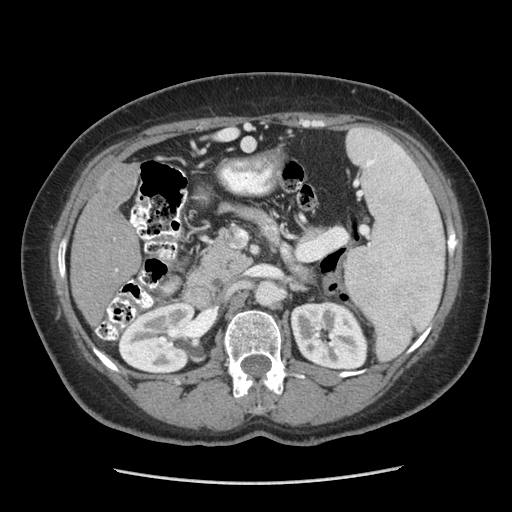
Contrast-enhanced abdominal CT (liver protocol), one axial slice. Slice 135 of 185 in the series (ordered by position). Soft-tissue window (W 400 / L 40 HU). 2.5 mm slice thickness. 512 × 512 image matrix, field of view 360 × 360 mm. Case-level facts recorded for this patient, not image findings: diagnosis: hepatocellular carcinoma (patient treated with transarterial chemoembolisation; whether this scan precedes or follows treatment is not stated here); TNM stage (as recorded): Stage-I; Child-Pugh class: A; tumour nodularity: uninodular.
Outlined on this slice (semi-automatic segmentation, software-assisted and operator-edited):
- liver parenchyma outside the tumour (the mass and vessels are separate outlines, so this box may not span the whole liver): bounding box (x1, y1, x2, y2) in pixels: (70, 164, 140, 320)
- mass: (99, 162, 137, 210)
- liver vessels: (115, 269, 118, 271)